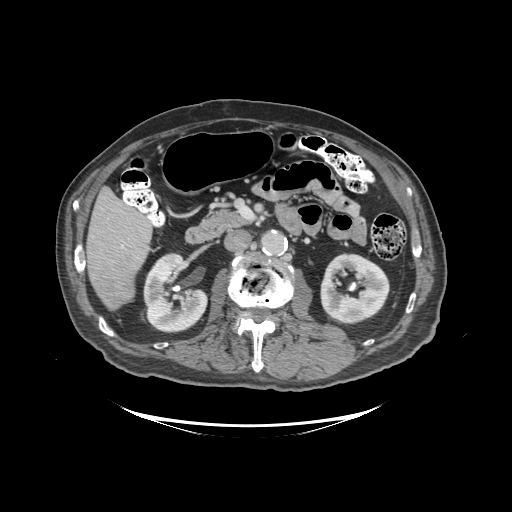
Contrast-enhanced abdominal CT (liver protocol), one axial slice. Position 40 of 99 along the scan axis. Reconstruction kernel STANDARD. 140 kVp. Soft-tissue window (W 400 / L 40 HU). 512 × 512 image matrix. From the clinical record (not read from this slice): diagnosis: hepatocellular carcinoma (patient treated with transarterial chemoembolisation; whether this scan precedes or follows treatment is not stated here); TNM stage (as recorded): Stage-I; Child-Pugh class: A; tumour nodularity: uninodular.
Annotated regions visible in this slice (semi-automatic segmentation, software-assisted and operator-edited):
- liver parenchyma outside the tumour (the mass and vessels are separate outlines, so this box may not span the whole liver): bounding box (x1, y1, x2, y2) in pixels: (86, 188, 152, 310)
- mass: (91, 259, 132, 307)
- liver vessels: (121, 245, 124, 248)